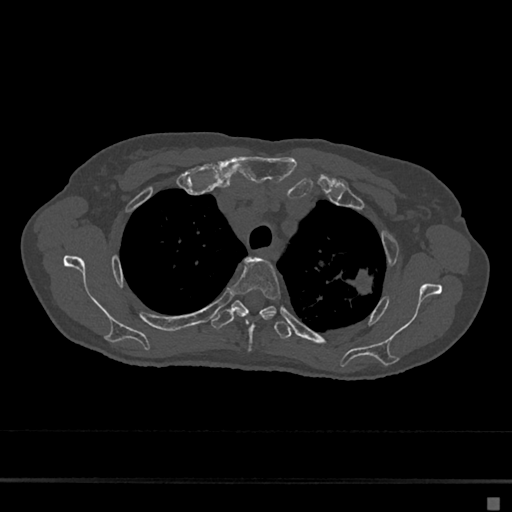
CT including the spine, one axial slice; slice 526 of 797 in the series (ordered by position); reconstruction kernel Br40s/3; 120 kVp; bone window (W 1800 / L 400 HU); 0.5 mm slice thickness; 512 × 512 image matrix, field of view 360 × 360 mm. Patient: female, 68 years. From the clinical record (not read from this slice): primary cancer: renal.
Structures marked on this image (semi-automatically segmented with operator editing):
- T3 vertebra: box from (x=231, y=258) to (x=281, y=349) px
- T4 vertebra: (x=211, y=300)–(x=291, y=340)